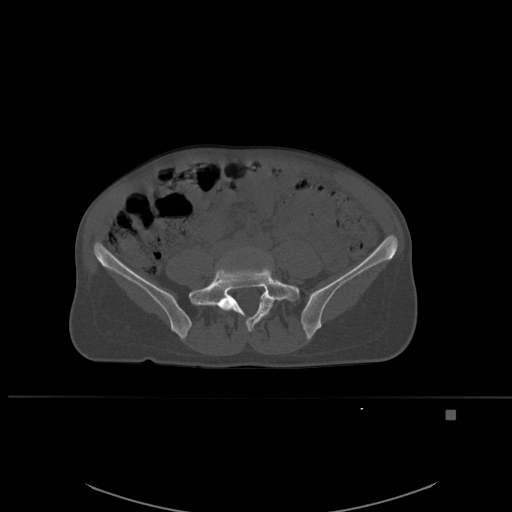
CT including the spine, one axial slice; slice 176 of 537 in the series (ordered by position); bone window (W 1800 / L 400 HU); 1.5 mm slice thickness; 512 × 512 image matrix, field of view 440 × 440 mm. Patient: female, 45 years. Case-level facts recorded for this patient, not image findings: primary cancer: lung.
Outlined on this slice (semi-automatically segmented with operator editing):
- L4 vertebra: bounding box <241,249,257,253> (left, top, right, bottom; pixels)
- L5 vertebra: <196,260,300,332>